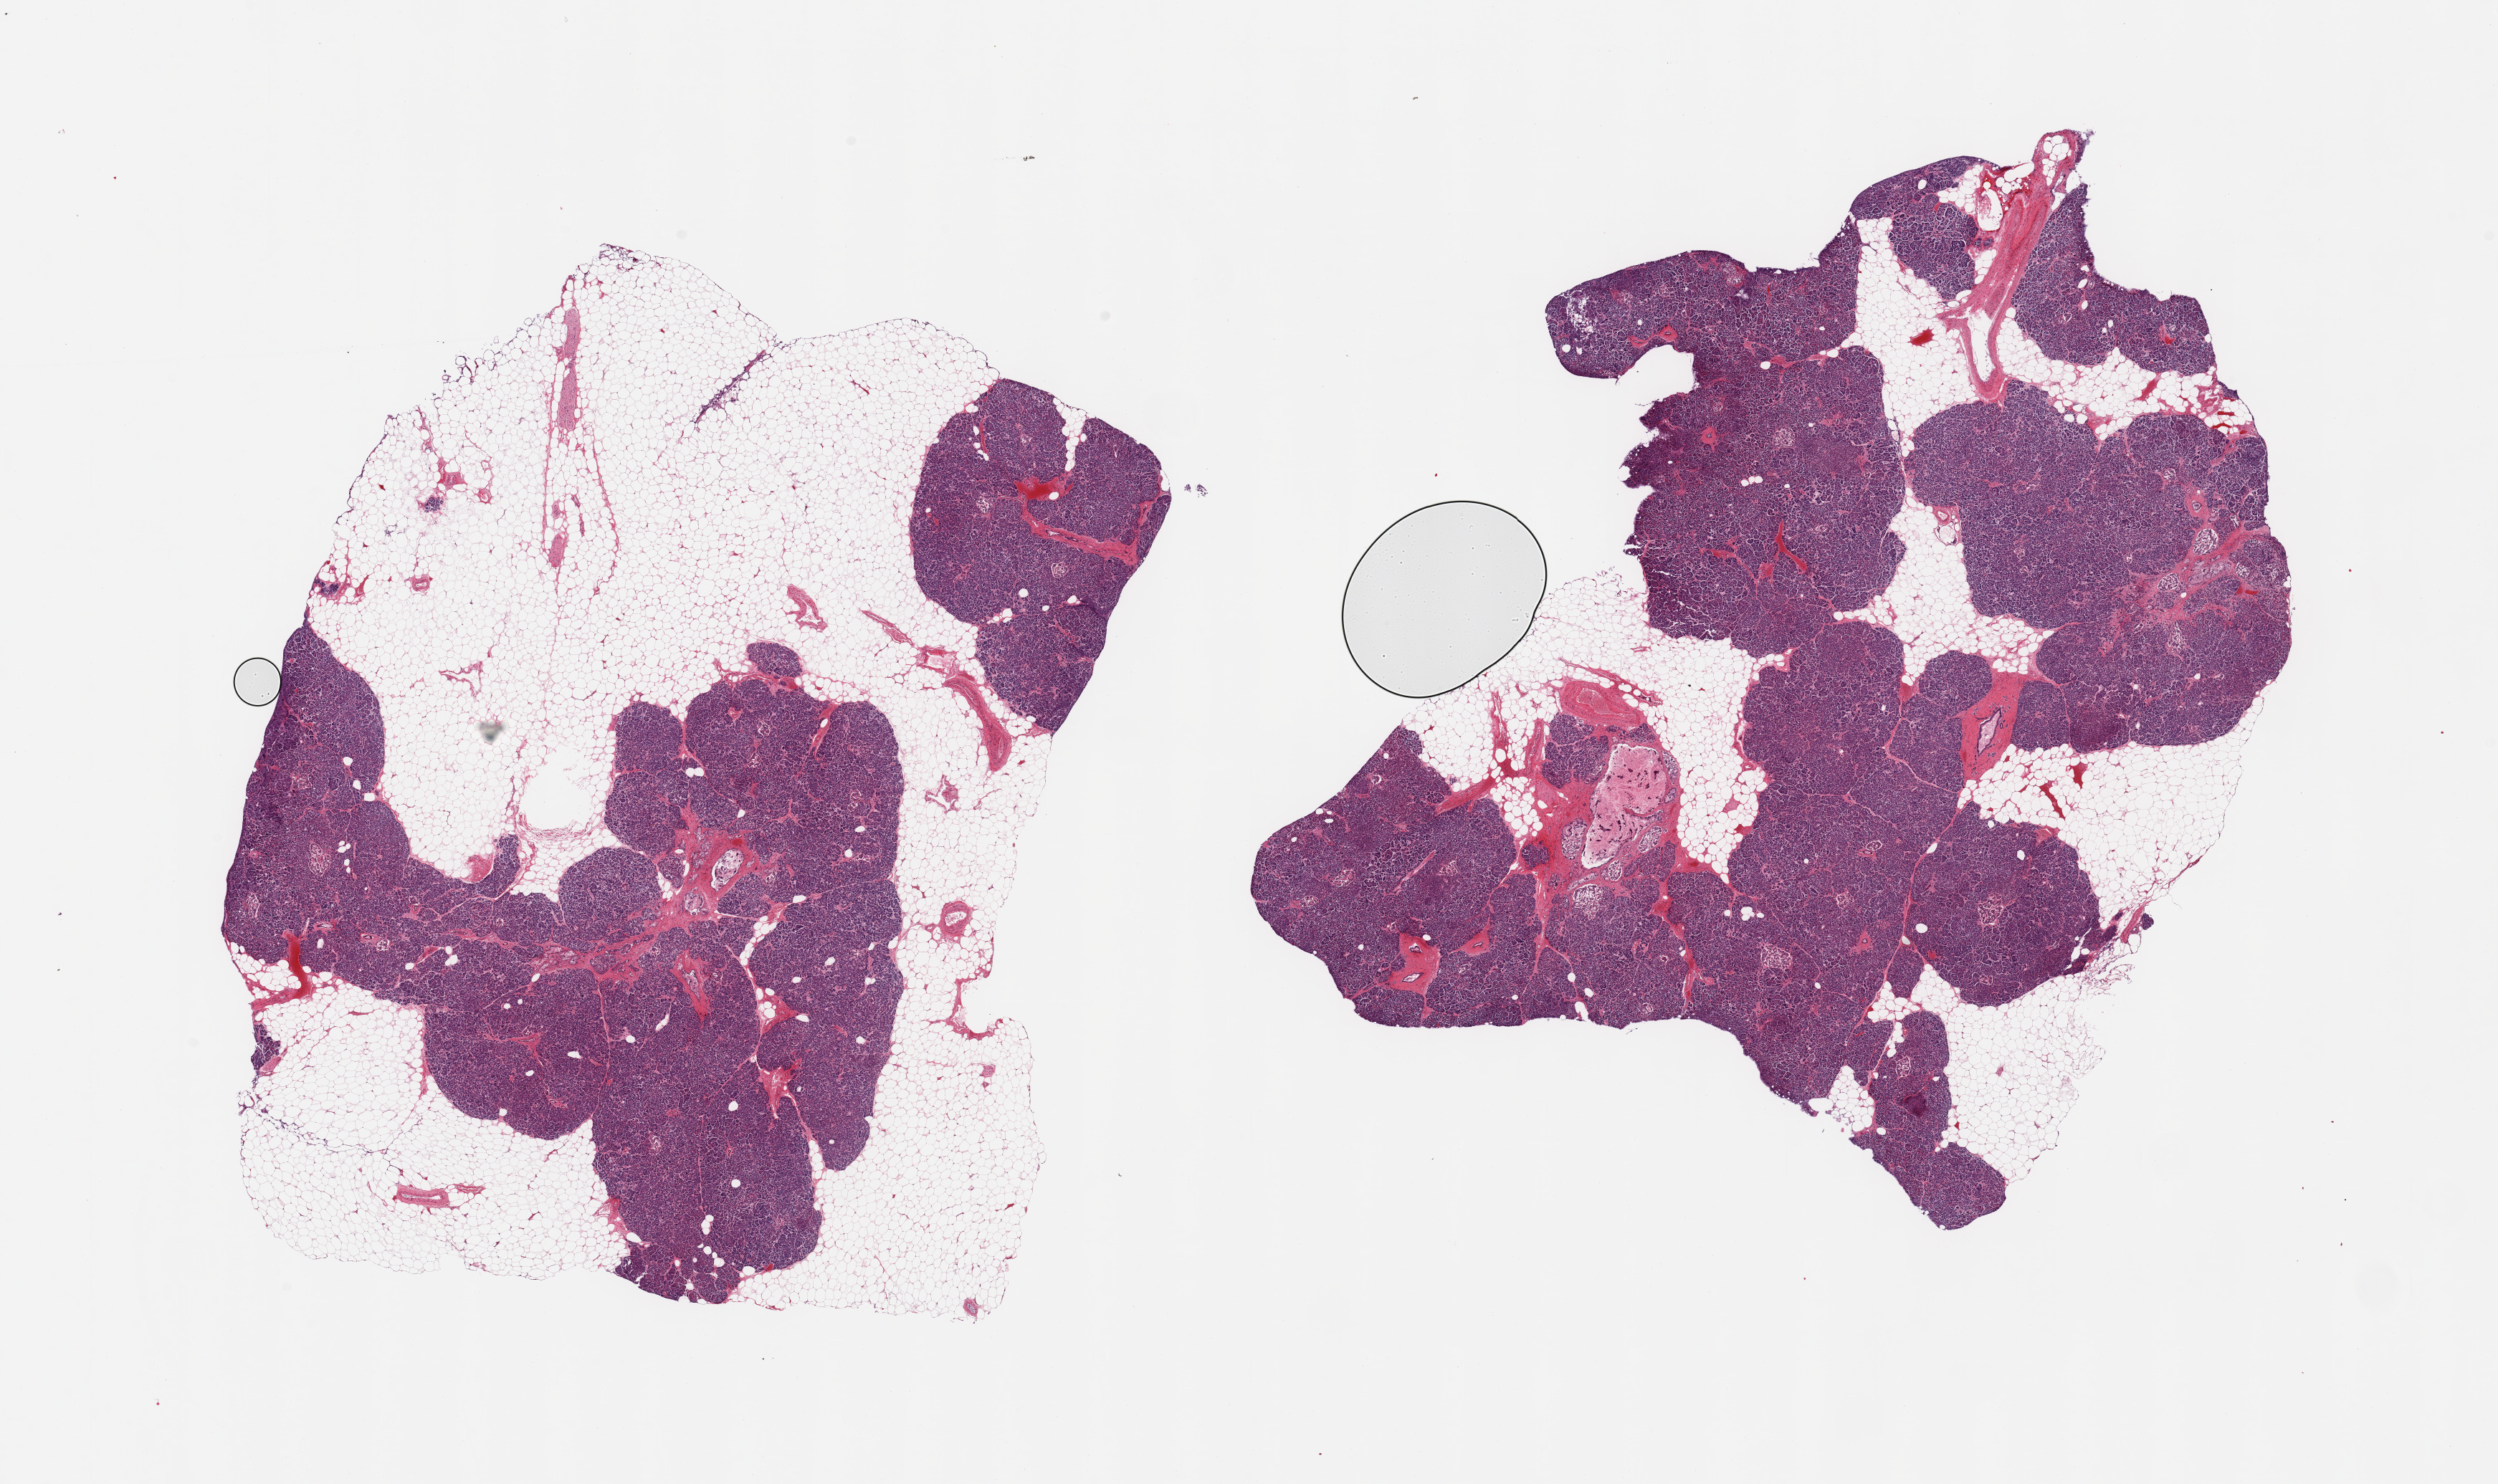
Digitized haematoxylin and eosin-stained section, brightfield, low-resolution overview of the scanned area, about 27.6 x 16.4 mm; PAXgene-fixed paraffin-embedded (PFPE) section; sampled site (target tissue): pancreas; donor tissue sample. Donor sex: male.
Review note (as recorded): 2 pieces, moderately advanced saponification, Islets degrading, barely visible.